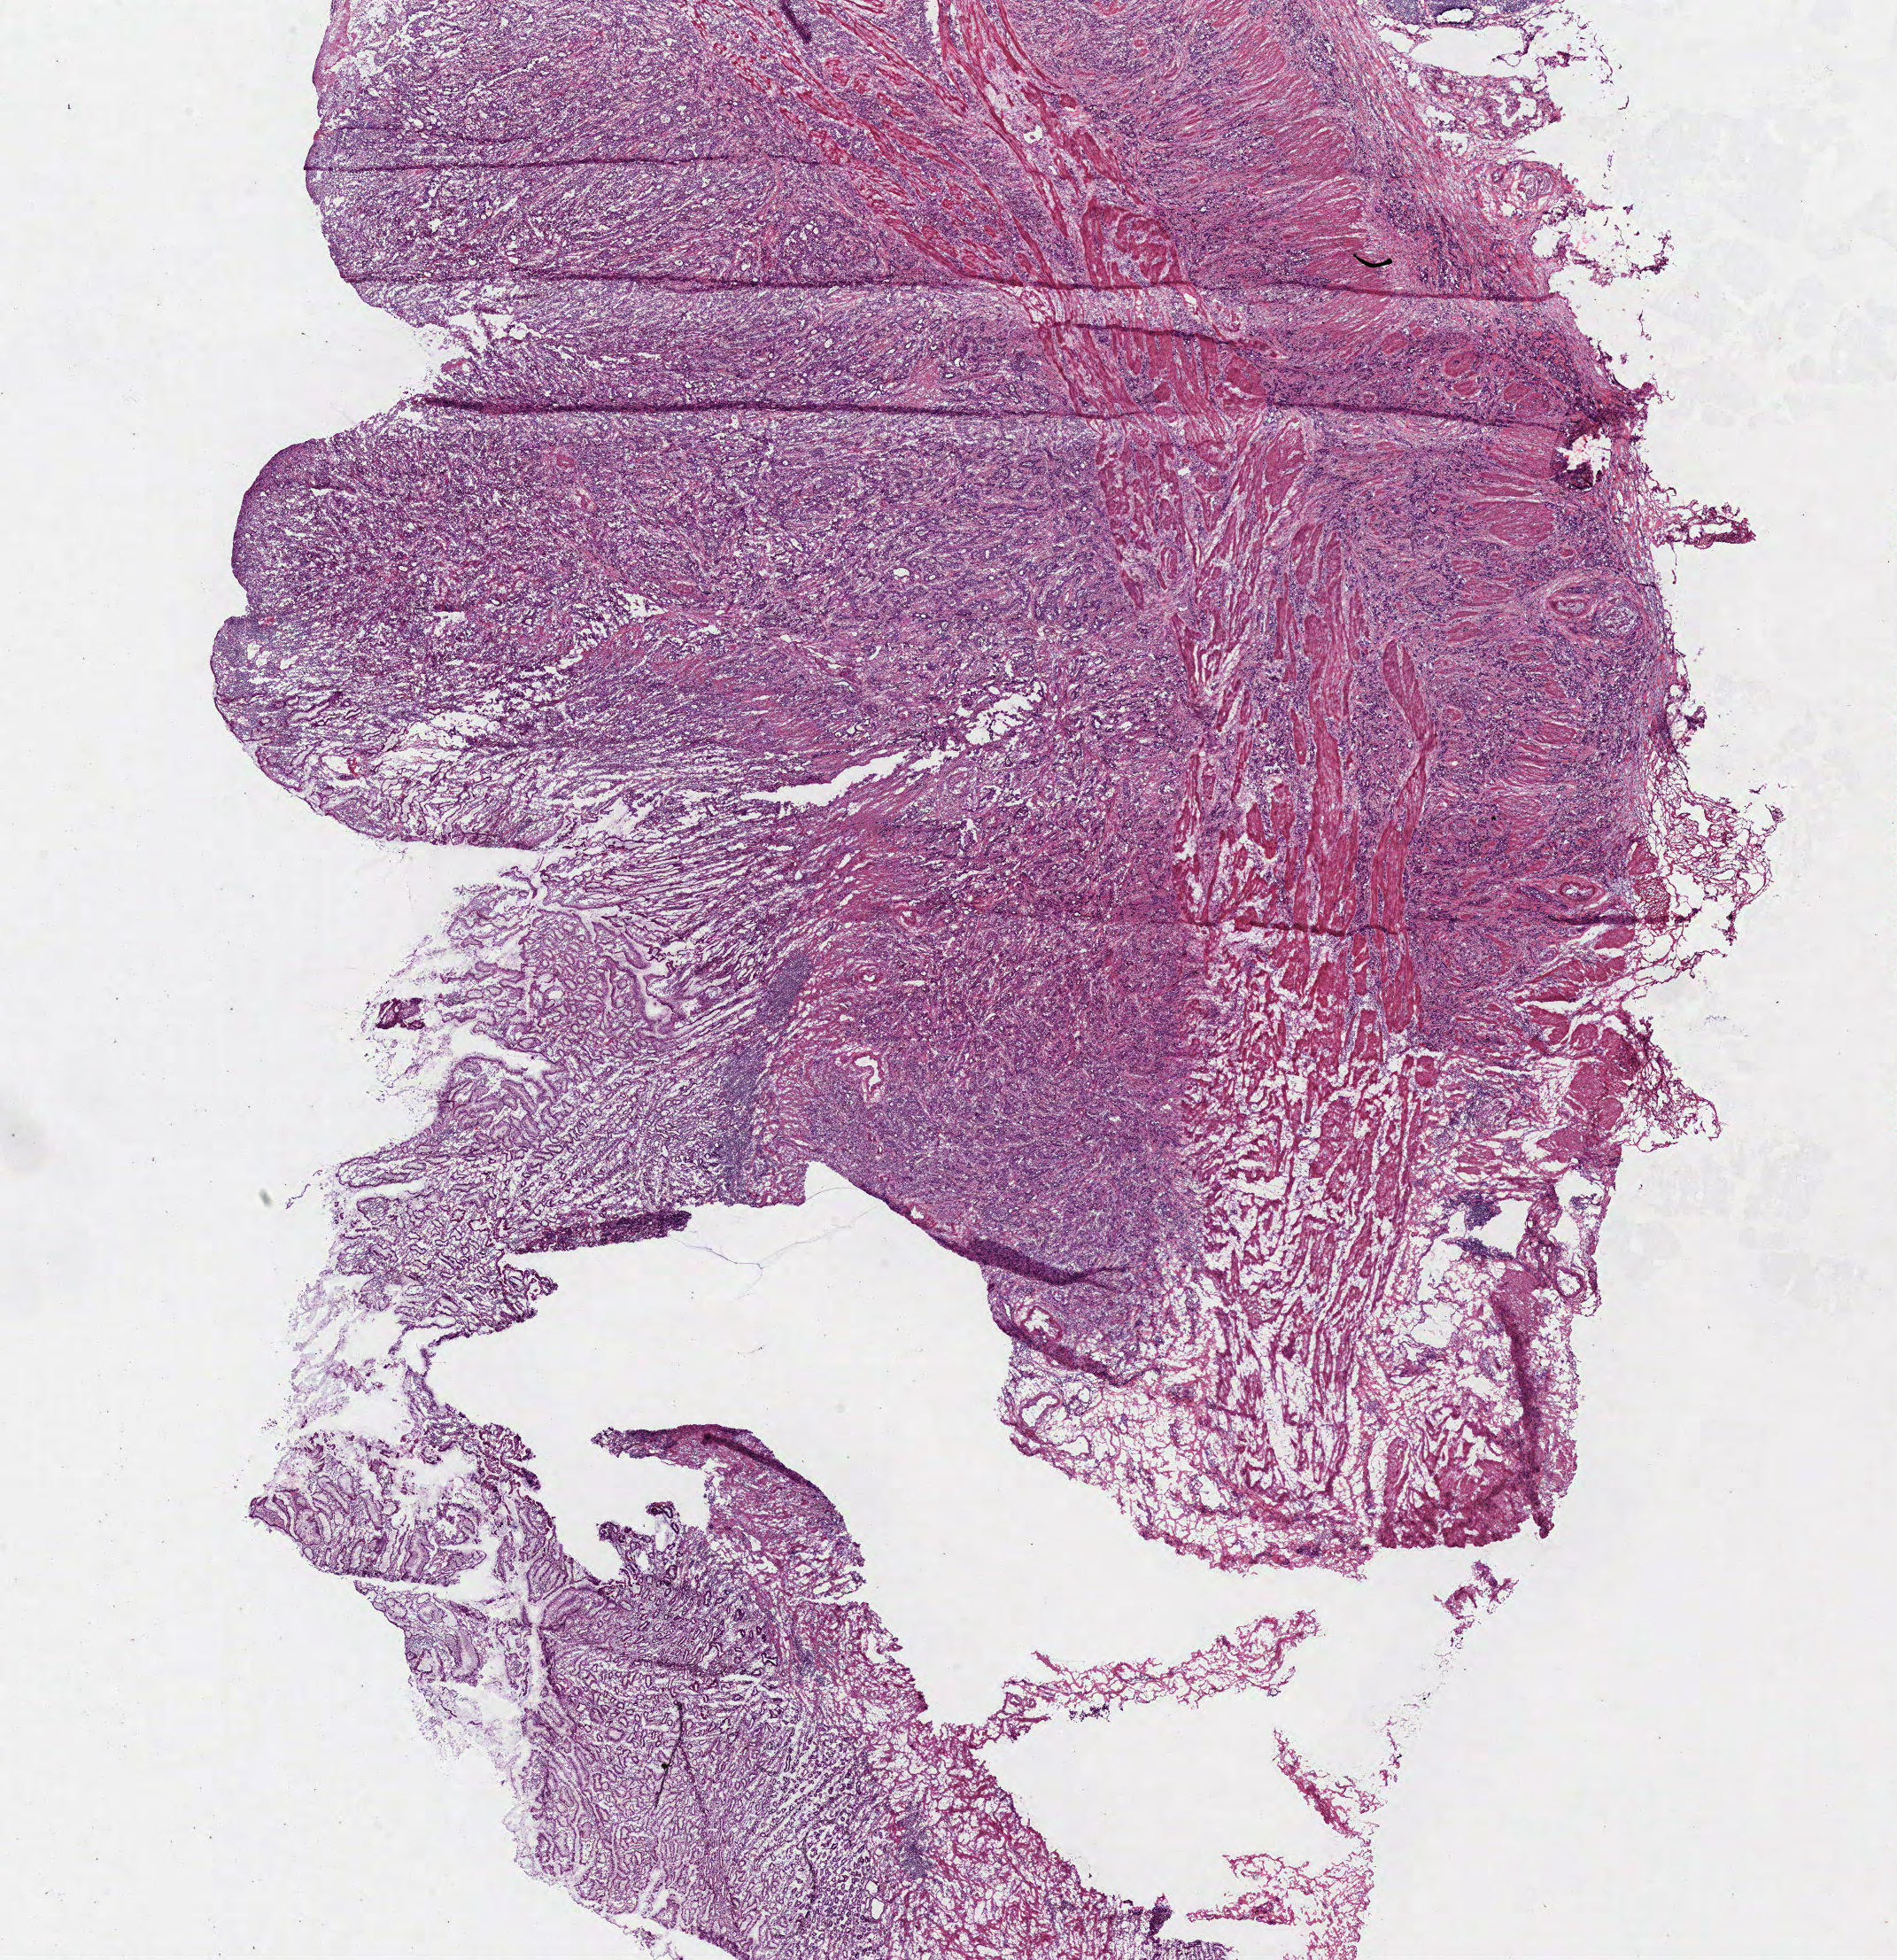
Whole-slide histology image, H&E-stained — a low-resolution overview of the entire scanned area, about 16.9 x 17.4 mm; frozen section from the bottom of the tissue portion; primary tumour sample from the stomach. Female, age 74 years at initial diagnosis. Histologic grade: G2 (moderately differentiated). Pathologist review of this section (percent, as recorded): tumour cells 90%, tumour nuclei 80%, normal cells 5%, stromal cells 5%, necrosis 0%. Inflammatory infiltration, as recorded: lymphocyte infiltration 10%, monocyte infiltration 0%, neutrophil infiltration 0%.
Lymph nodes positive (case pathology): 2 of 4 examined. Pathologic diagnosis: Adenocarcinoma, NOS (body of stomach). AJCC pathologic stage: IIB (7th edition).